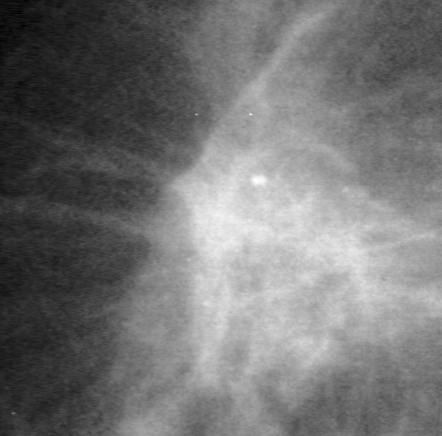
Cropped region of a digitized screen-film mammogram centred on a radiologist-marked abnormality, left breast, MLO view, BI-RADS breast density category 2 (scale 1–4).
- Marked abnormality: mass, shape irregular, margins spiculated; BI-RADS assessment category 5; pathology (as recorded): malignant.